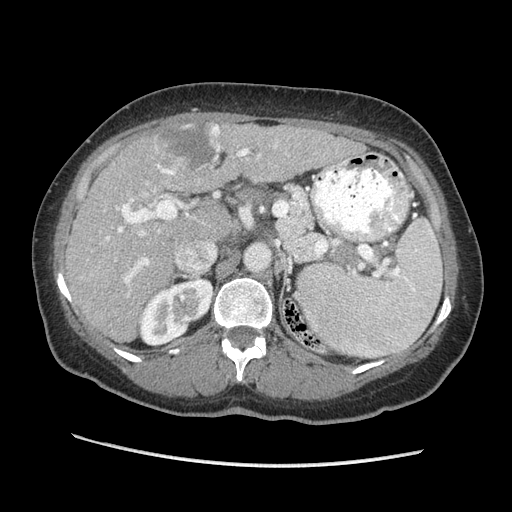
Contrast-enhanced abdominal CT (liver protocol), one axial slice. Slice 130 of 170 in the series (ordered by position). Reconstruction kernel STANDARD. 140 kVp. Soft-tissue window (W 400 / L 40 HU). 2.5 mm slice thickness. 512 × 512 image matrix, field of view 360 × 360 mm. From the clinical record (not read from this slice): diagnosis: hepatocellular carcinoma (patient treated with transarterial chemoembolisation; whether this scan precedes or follows treatment is not stated here); TNM stage (as recorded): Stage-II; Child-Pugh class: A.
Structures marked on this image (semi-automatic segmentation, software-assisted and operator-edited):
- liver parenchyma outside the tumour (the mass and vessels are separate outlines, so this box may not span the whole liver): box from (x=66, y=122) to (x=364, y=342) px
- mass: (x=154, y=119)–(x=221, y=176)
- liver vessels: (x=106, y=144)–(x=277, y=295)